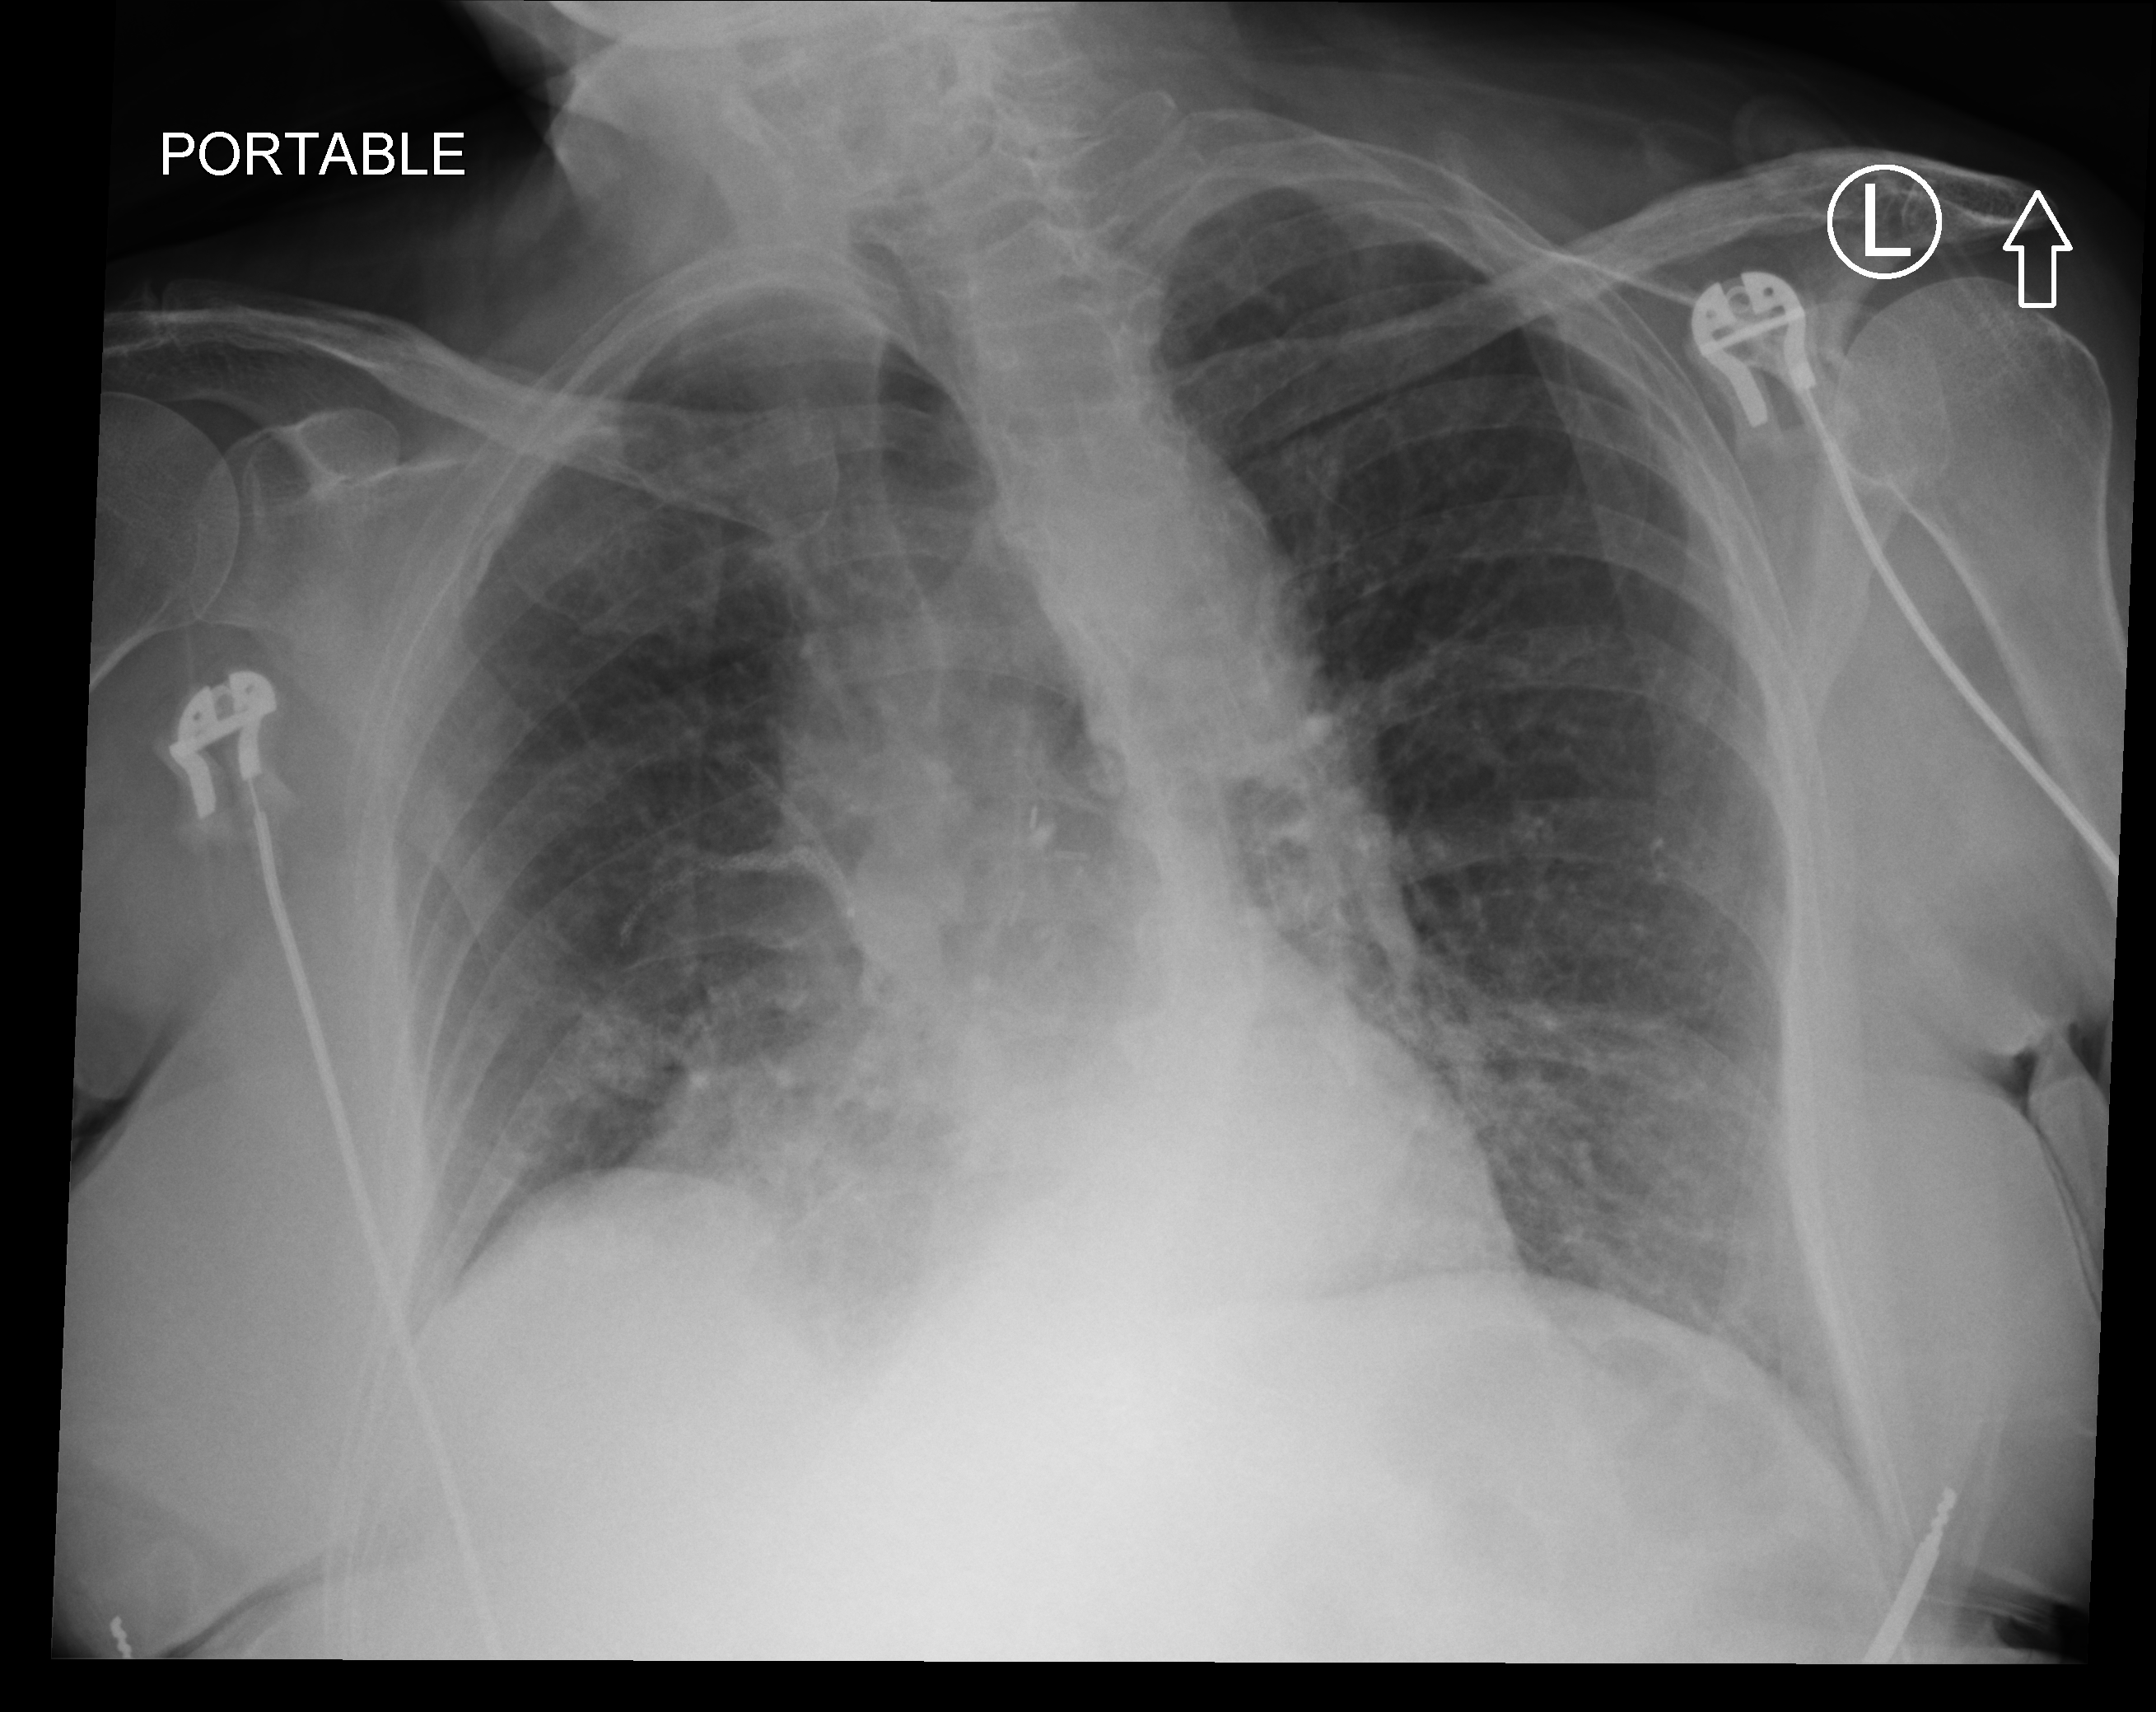
Portable chest radiograph; anteroposterior (AP) projection. Female patient hospitalised with COVID-19, age 75–90 years.
From the hospital-stay record, not from the radiograph (when in the stay this image was taken is not recorded): chronic kidney disease (admission record): no; admitted to intensive care during this hospital stay: no.